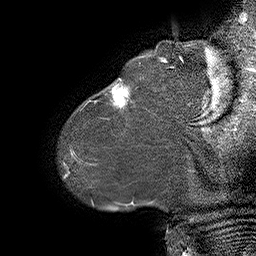
Breast MRI (dynamic contrast-enhanced), one sagittal slice. Position 5 of 55 along the scan axis. Dynamic contrast-enhanced series, time point 2 of 6 at this slice position (early post-contrast). 1.5 T. TE 4.5 ms, TR 32.4 ms. 256 × 256 image matrix. Female patient. Case-level facts recorded for this patient, not image findings: setting: breast cancer imaged before/during neoadjuvant chemotherapy; receptor status: HER2-positive.
Annotated regions visible in this slice (semi-automatic segmentation, software-assisted and operator-edited):
- analysis volume of interest (the breast-tissue region the enhancement analysis was run in; not a lesion): bounding box <80,64,163,134> (left, top, right, bottom; pixels)
- tumour enhancement mask (voxels above the 100 % enhancement threshold inside the analysis volume of interest): <110,83,129,108>